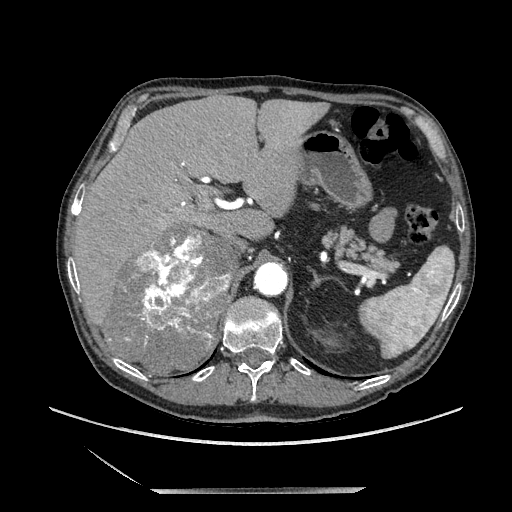
Contrast-enhanced abdominal CT, one axial slice. Slice 146 of 243 in the series (ordered by position). Soft-tissue window (W 400 / L 40 HU). 512 × 512 image matrix, field of view 420 × 420 mm. Male patient. Case-level facts recorded for this patient, not image findings: diagnosis: adrenocortical carcinoma; tumour side: right adrenal; tumour size at pathology: 16 cm.
Outlined on this slice (semi-automatically segmented with operator editing):
- mass: bounding box (x1, y1, x2, y2) in pixels: (106, 224, 230, 375)